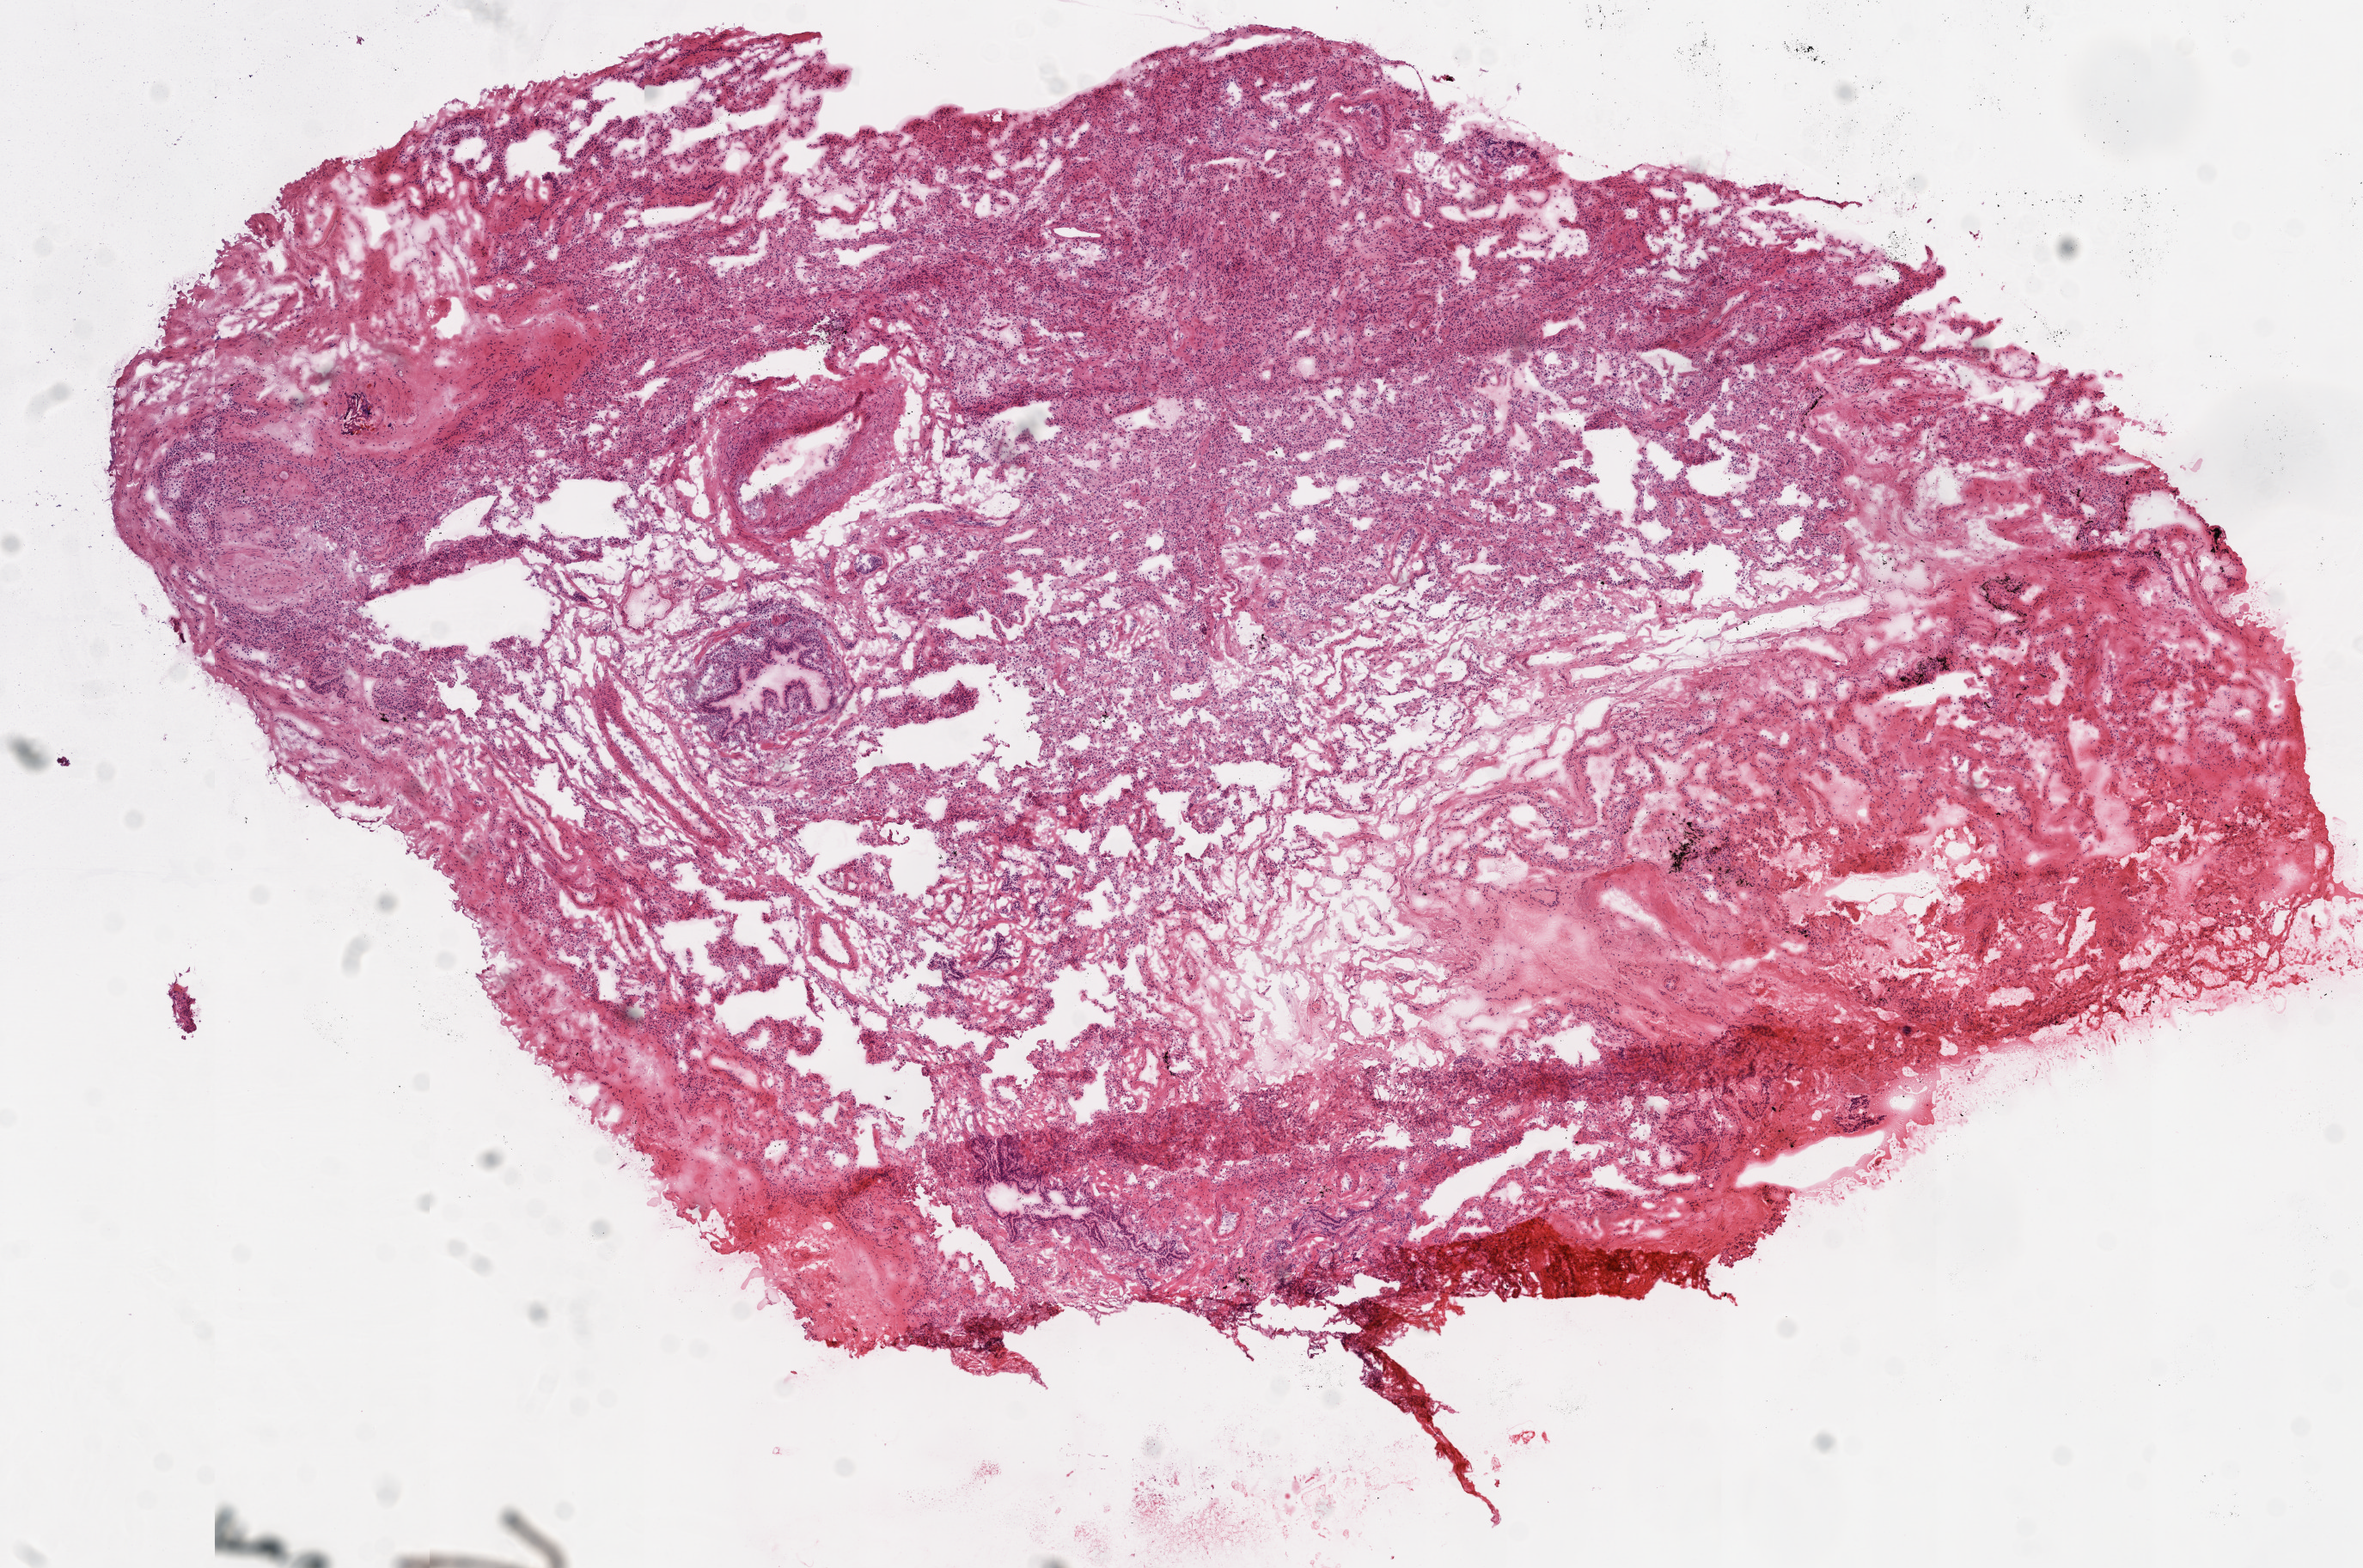
Hematoxylin and eosin (H&E) stained whole-slide image — shown as a low-resolution overview of the whole scanned area (about 11.0 x 7.3 mm, acquisition: 20x scan). Frozen section from the top of the tissue portion. Lung, solid tissue normal (non-tumour tissue) sample. Patient: male, age at initial diagnosis 55 years.
This section: solid tissue normal (non-tumour) sample from the same patient. Patient diagnosis: Squamous cell carcinoma, NOS (lower lobe, lung).